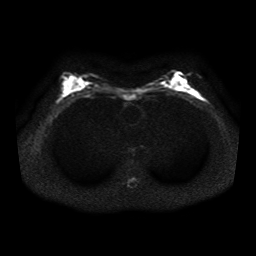
Breast MRI, one axial slice. Slice 22 of 41 in the series (ordered by position). Diffusion-weighted series; image 2 of 4 stored at this slice position (different b-values; order by instance number). 1.5 T. 256 × 256 image matrix. Female patient.
Annotated regions visible in this slice (manually delineated by an expert):
- tumour on diffusion-weighted imaging: bounding box (x1, y1, x2, y2) in pixels: (196, 94, 201, 99)